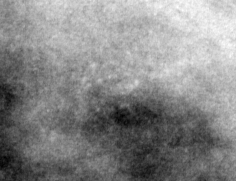
Region of interest cut from a scanned film mammogram (one marked finding); right breast; CC view.
Calcifications, morphology pleomorphic, distribution clustered; BI-RADS assessment category 4; pathology result (as recorded, not read from the image): malignant.